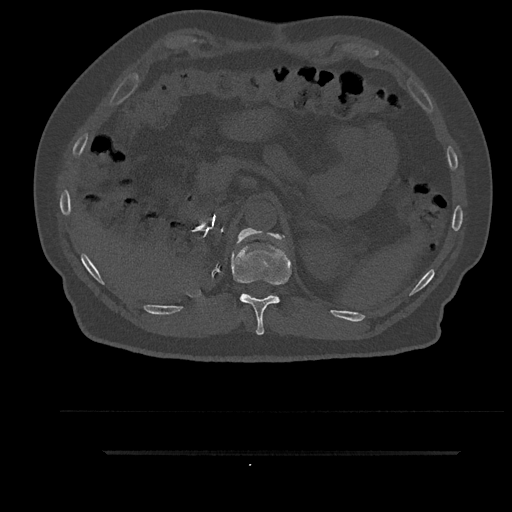
CT including the spine, one axial slice. Slice 288 of 797 in the series (ordered by position). Bone window (W 1800 / L 400 HU). 512 × 512 image matrix. Patient: male, 63 years. Case-level facts recorded for this patient, not image findings: primary cancer: renal; vertebrae with lytic lesions (as recorded): T8.
Structures marked on this image (semi-automatic segmentation, software-assisted and operator-edited):
- T11 vertebra: box from (x=231, y=228) to (x=292, y=335) px
- T12 vertebra: (x=238, y=228)–(x=261, y=244)